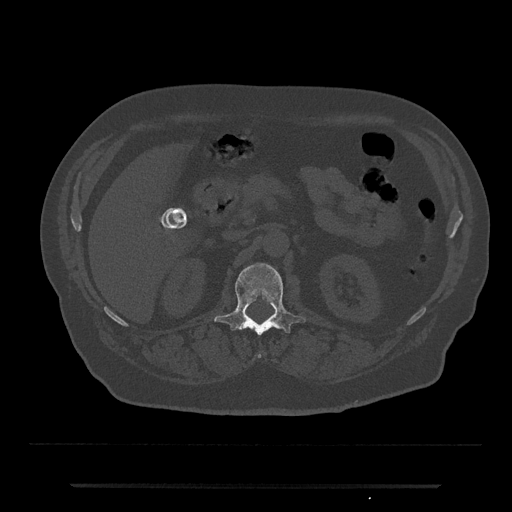
CT including the spine, one axial slice; position 539 of 797 along the scan axis; reconstruction kernel Br40s/3; 120 kVp; bone window (W 1800 / L 400 HU); 0.5 mm slice thickness; 512 × 512 image matrix. Patient: male, 80 years. From the clinical record (not read from this slice): primary cancer: prostate; vertebrae with lytic lesions (as recorded): L1, T11.
Structures marked on this image (semi-automatically segmented with operator editing):
- L1 vertebra: box from (x=214, y=263) to (x=305, y=358) px